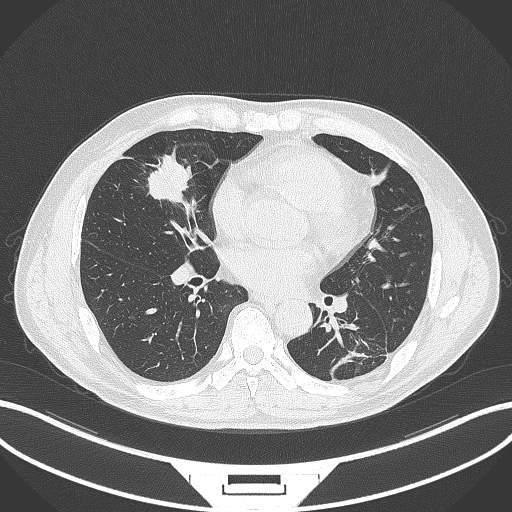
Chest CT, one axial slice. Position 135 of 399 along the scan axis. Reconstruction kernel B70f. 120 kVp. Lung window (W 1500 / L -600 HU). 1 mm slice thickness. 512 × 512 image matrix, field of view 400 × 400 mm. Male patient, age 59 years. Case-level facts recorded for this patient, not image findings: clinical TNM (as recorded): T2a N1 M0.
Outlined on this slice (rectangle marked by the reading radiologist):
- lung tumour (recorded histology: adenocarcinoma): bounding box <144,150,196,207> (left, top, right, bottom; pixels)